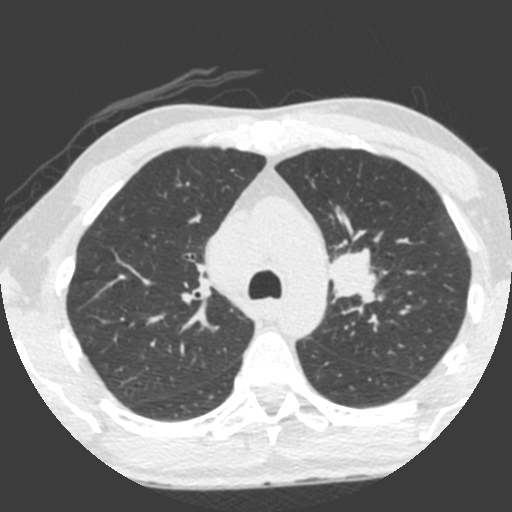
Axial slice from a low-dose chest CT screening exam. Third screening round (two years after baseline). Lung window (W 1500 / L -600 HU). Slice 153 of 212 in the series. 512 × 512 image matrix. Male, age 55 years at enrolment. Current smoker at enrolment.
Expert reader's lesion annotation, bounding box <308,233,388,322> (left, top, right, bottom; pixels). The exam's reader record, not a measurement of the box and not confirmed to be the same lesion: non-calcified nodule or mass ≥4 mm, left upper lobe, 49 × 29 mm, spiculated (stellate) margins, soft tissue attenuation, pre-existing on the prior screen: yes; interval growth: yes. Official screen result: positive, other. Lung cancer was diagnosed 0 days after this screen: small cell carcinoma, NOS, left upper lobe, undifferentiated (G4), stage IV (AJCC 6th edition), 60 mm at pathology.